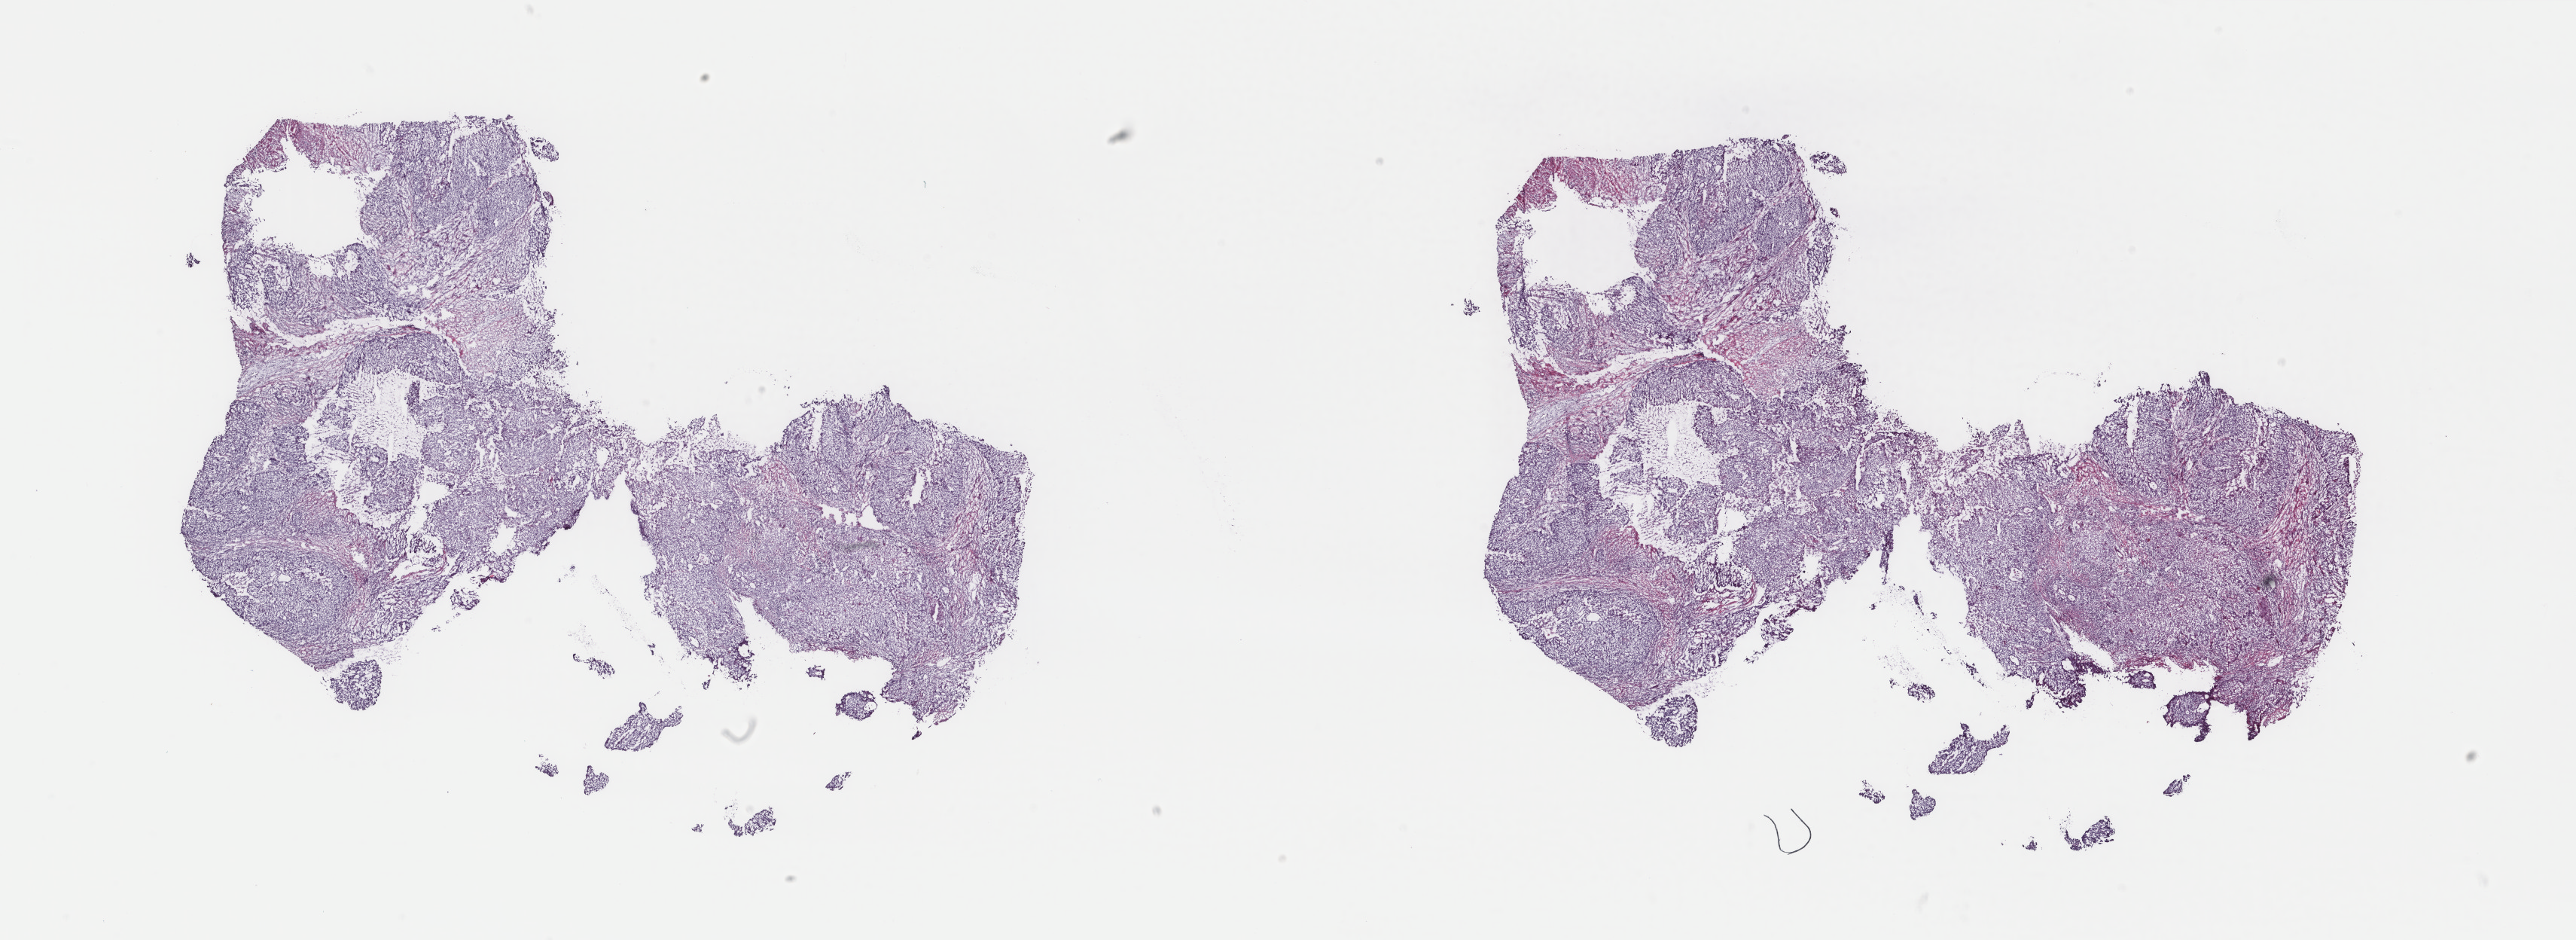
Whole-slide histology image, Hematoxylin and eosin (H&E) stained — shown as a low-resolution overview of the whole scanned area (about 27.2 x 9.9 mm), frozen section, uterus, primary tumour sample. Female, age 64 years at initial diagnosis. Histologic grade: G3 (poorly differentiated). Pathologist review of this section (percent, as recorded): tumour cells 85%, tumour nuclei 75%, normal cells 0%, stromal cells 15%, necrosis 0%. Inflammatory infiltration, as recorded: lymphocyte infiltration 0%, monocyte infiltration 0%, neutrophil infiltration 0%.
• diagnosis: Endometrioid adenocarcinoma, NOS (endometrium)
• lymph nodes positive (case pathology): 0 of 7 examined
• FIGO stage: IB